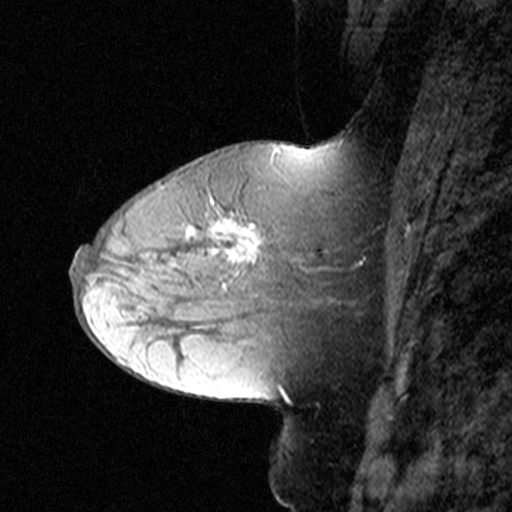
Breast MRI (dynamic contrast-enhanced), one sagittal slice. Position 19 of 44 along the scan axis. Dynamic contrast-enhanced study with each time point stored as its own series, time point 2 of 3 at this slice position (early post-contrast, ordered by acquisition time). 1.5 T. TE 4.5 ms, TR 11 ms. 3 mm slice thickness. 512 × 512 image matrix. Patient: female, 50 years. From the clinical record (not read from this slice): setting: breast cancer imaged before/during neoadjuvant chemotherapy; receptor status: HR-positive, HER2-negative.
Structures marked on this image (semi-automatic segmentation, software-assisted and operator-edited):
- analysis volume of interest (the breast-tissue region the enhancement analysis was run in; not a lesion): bounding box (x1, y1, x2, y2) in pixels: (180, 198, 338, 311)
- tumour enhancement mask (voxels above the 90 % enhancement threshold inside the analysis volume of interest): (188, 220, 306, 290)